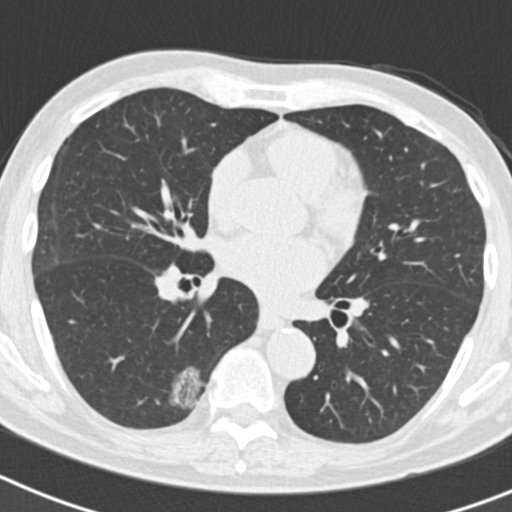
Chest CT (low-dose screening protocol), one axial image. Second annual screen. Lung window (W 1500 / L -600 HU). 2 mm slice thickness. Standard (soft-tissue) reconstruction kernel (B30f). 512 × 512 image matrix, field of view 300 × 300 mm. Male participant, aged 70 years at enrolment.
Expert reader's lesion annotation, bounding box [x1, y1, x2, y2] px = [127, 363, 205, 430]. The screening reader recorded 5 non-calcified nodules or masses ≥4 mm on this exam (right lower lobe, right lower lobe, right upper lobe, right upper lobe, left upper lobe); which of them this box marks is not recorded. Lung cancer was diagnosed 622 days after this screen: bronchiolo-alveolar adenocarcinoma, NOS, right lower lobe, poorly differentiated (G3), stage IB (AJCC 6th edition), 30 mm at pathology.